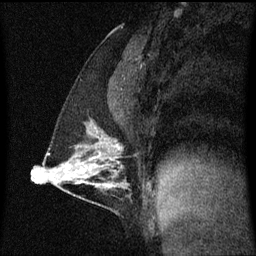
Breast MRI (dynamic contrast-enhanced), one sagittal slice; slice 33 of 60 in the series (ordered by position); dynamic contrast-enhanced series, image 2 of 3 at this slice position (ordered by acquisition); 1.5 T; TE 4.2 ms, TR 8.4 ms; 2 mm slice thickness; 256 × 256 image matrix, field of view 200 × 200 mm. Patient: female, 40 years. From the clinical record (not read from this slice): setting: breast cancer imaged before/during neoadjuvant chemotherapy; receptor status: triple-negative.
Annotated regions visible in this slice (semi-automatic segmentation, software-assisted and operator-edited):
- analysis volume of interest (the breast-tissue region the enhancement analysis was run in; not a lesion): bounding box (x1, y1, x2, y2) in pixels: (43, 120, 132, 195)
- tumour enhancement mask (voxels above the 70 % enhancement threshold inside the analysis volume of interest): (115, 144, 121, 149)